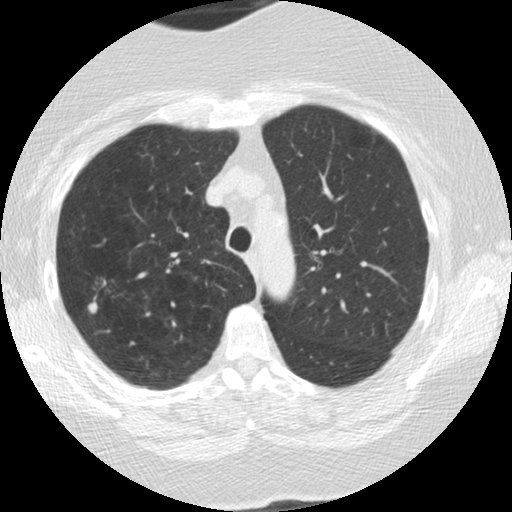
Low-dose screening chest CT, one axial slice. Slice 131 of 166 in the series (ordered by position). Reconstruction kernel STANDARD. Lung window (W 1500 / L -600 HU). 2.5 mm slice thickness. 512 × 512 image matrix, field of view 309 × 309 mm.
Structures marked on this image (expert manual segmentation):
- lesion 1 (tumor, upper lobe of right lung): bounding box (x1, y1, x2, y2) in pixels: (88, 301, 98, 313)